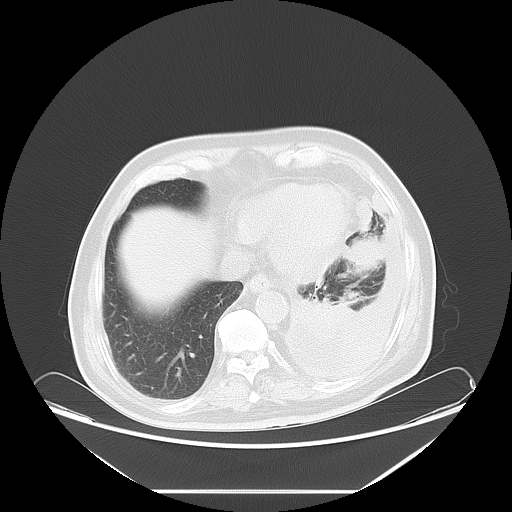
Chest CT, one axial slice; position 19 of 63 along the scan axis; reconstruction kernel LUNG; 120 kVp; lung window (W 1500 / L -600 HU); 5 mm slice thickness; 512 × 512 image matrix, field of view 448 × 448 mm. Patient: male, 67 years. From the clinical record (not read from this slice): clinical TNM (as recorded): T1b N1 M1a; histopathological grade: G3.
Annotated regions visible in this slice (bounding box drawn by a radiologist):
- lung tumour (recorded histology: small cell carcinoma): bounding box <343,233,387,278> (left, top, right, bottom; pixels)